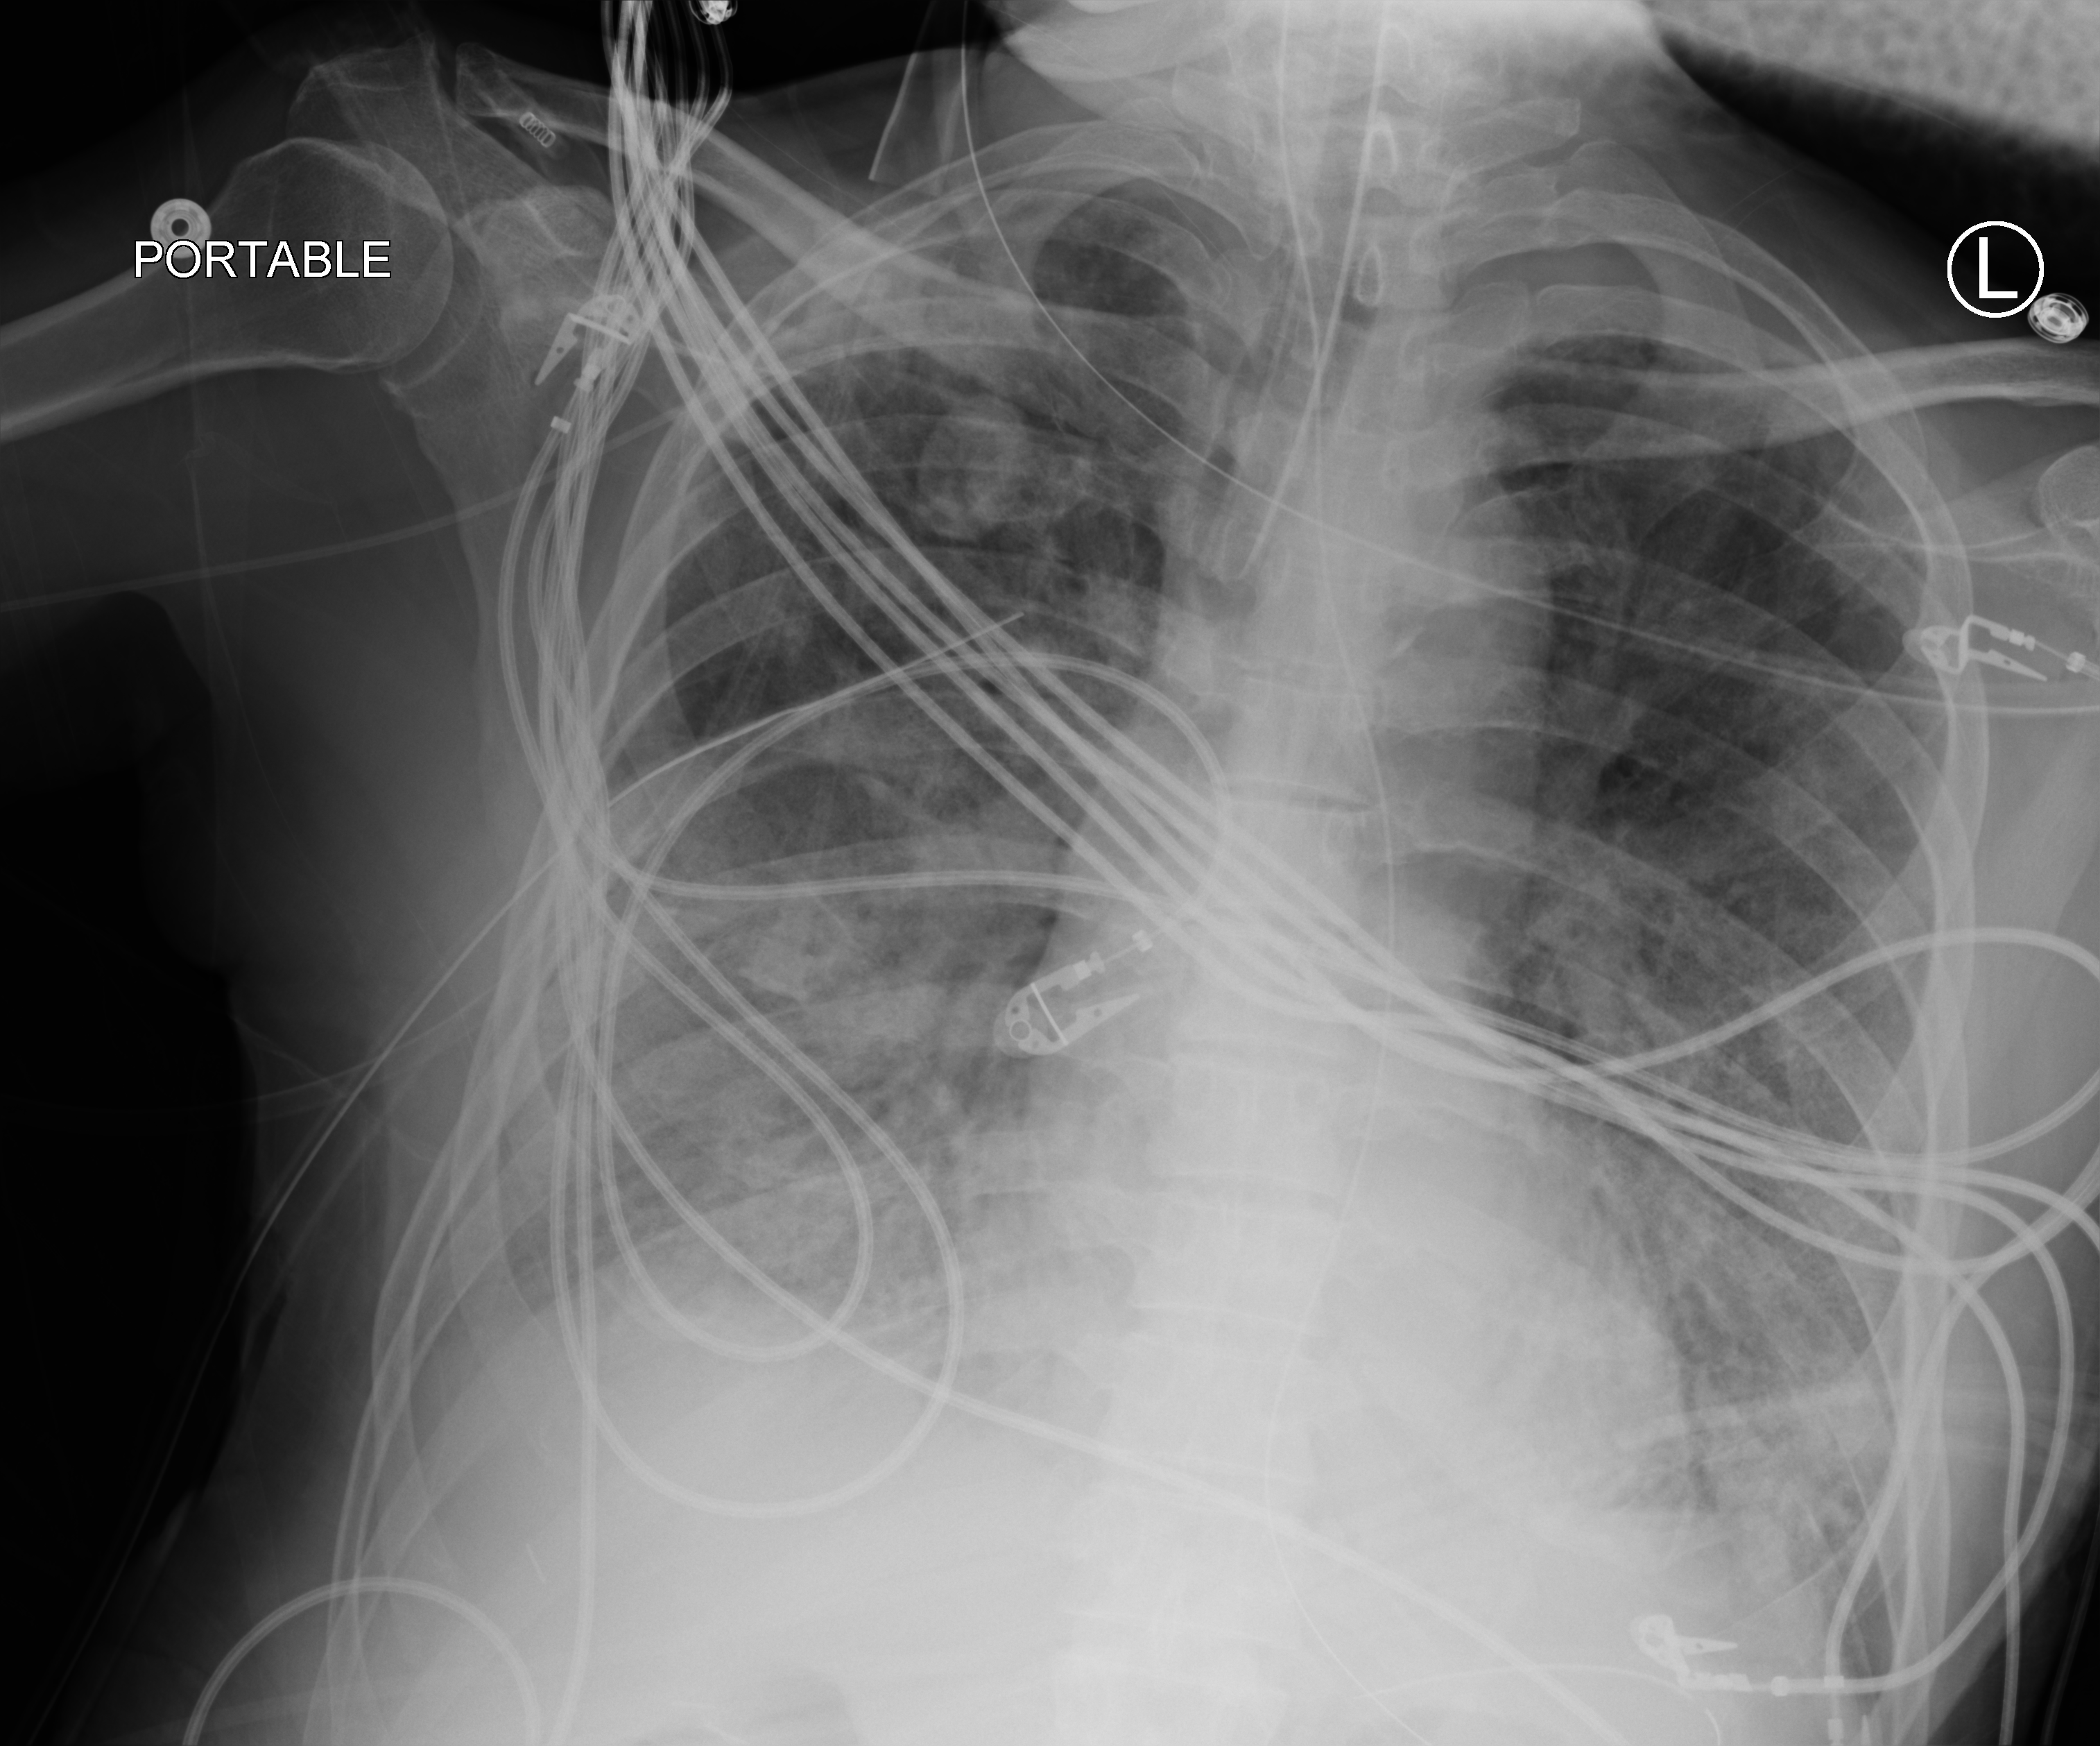
Chest X-ray (portable), anteroposterior (AP) projection. Patient hospitalised with COVID-19; male, aged 60–74 years.
Admission-level facts for this patient (not findings on this image; timing relative to this image not recorded): length of hospital stay: 31 days; other chronic lung disease (admission record): no; smoking status (admission record): former.